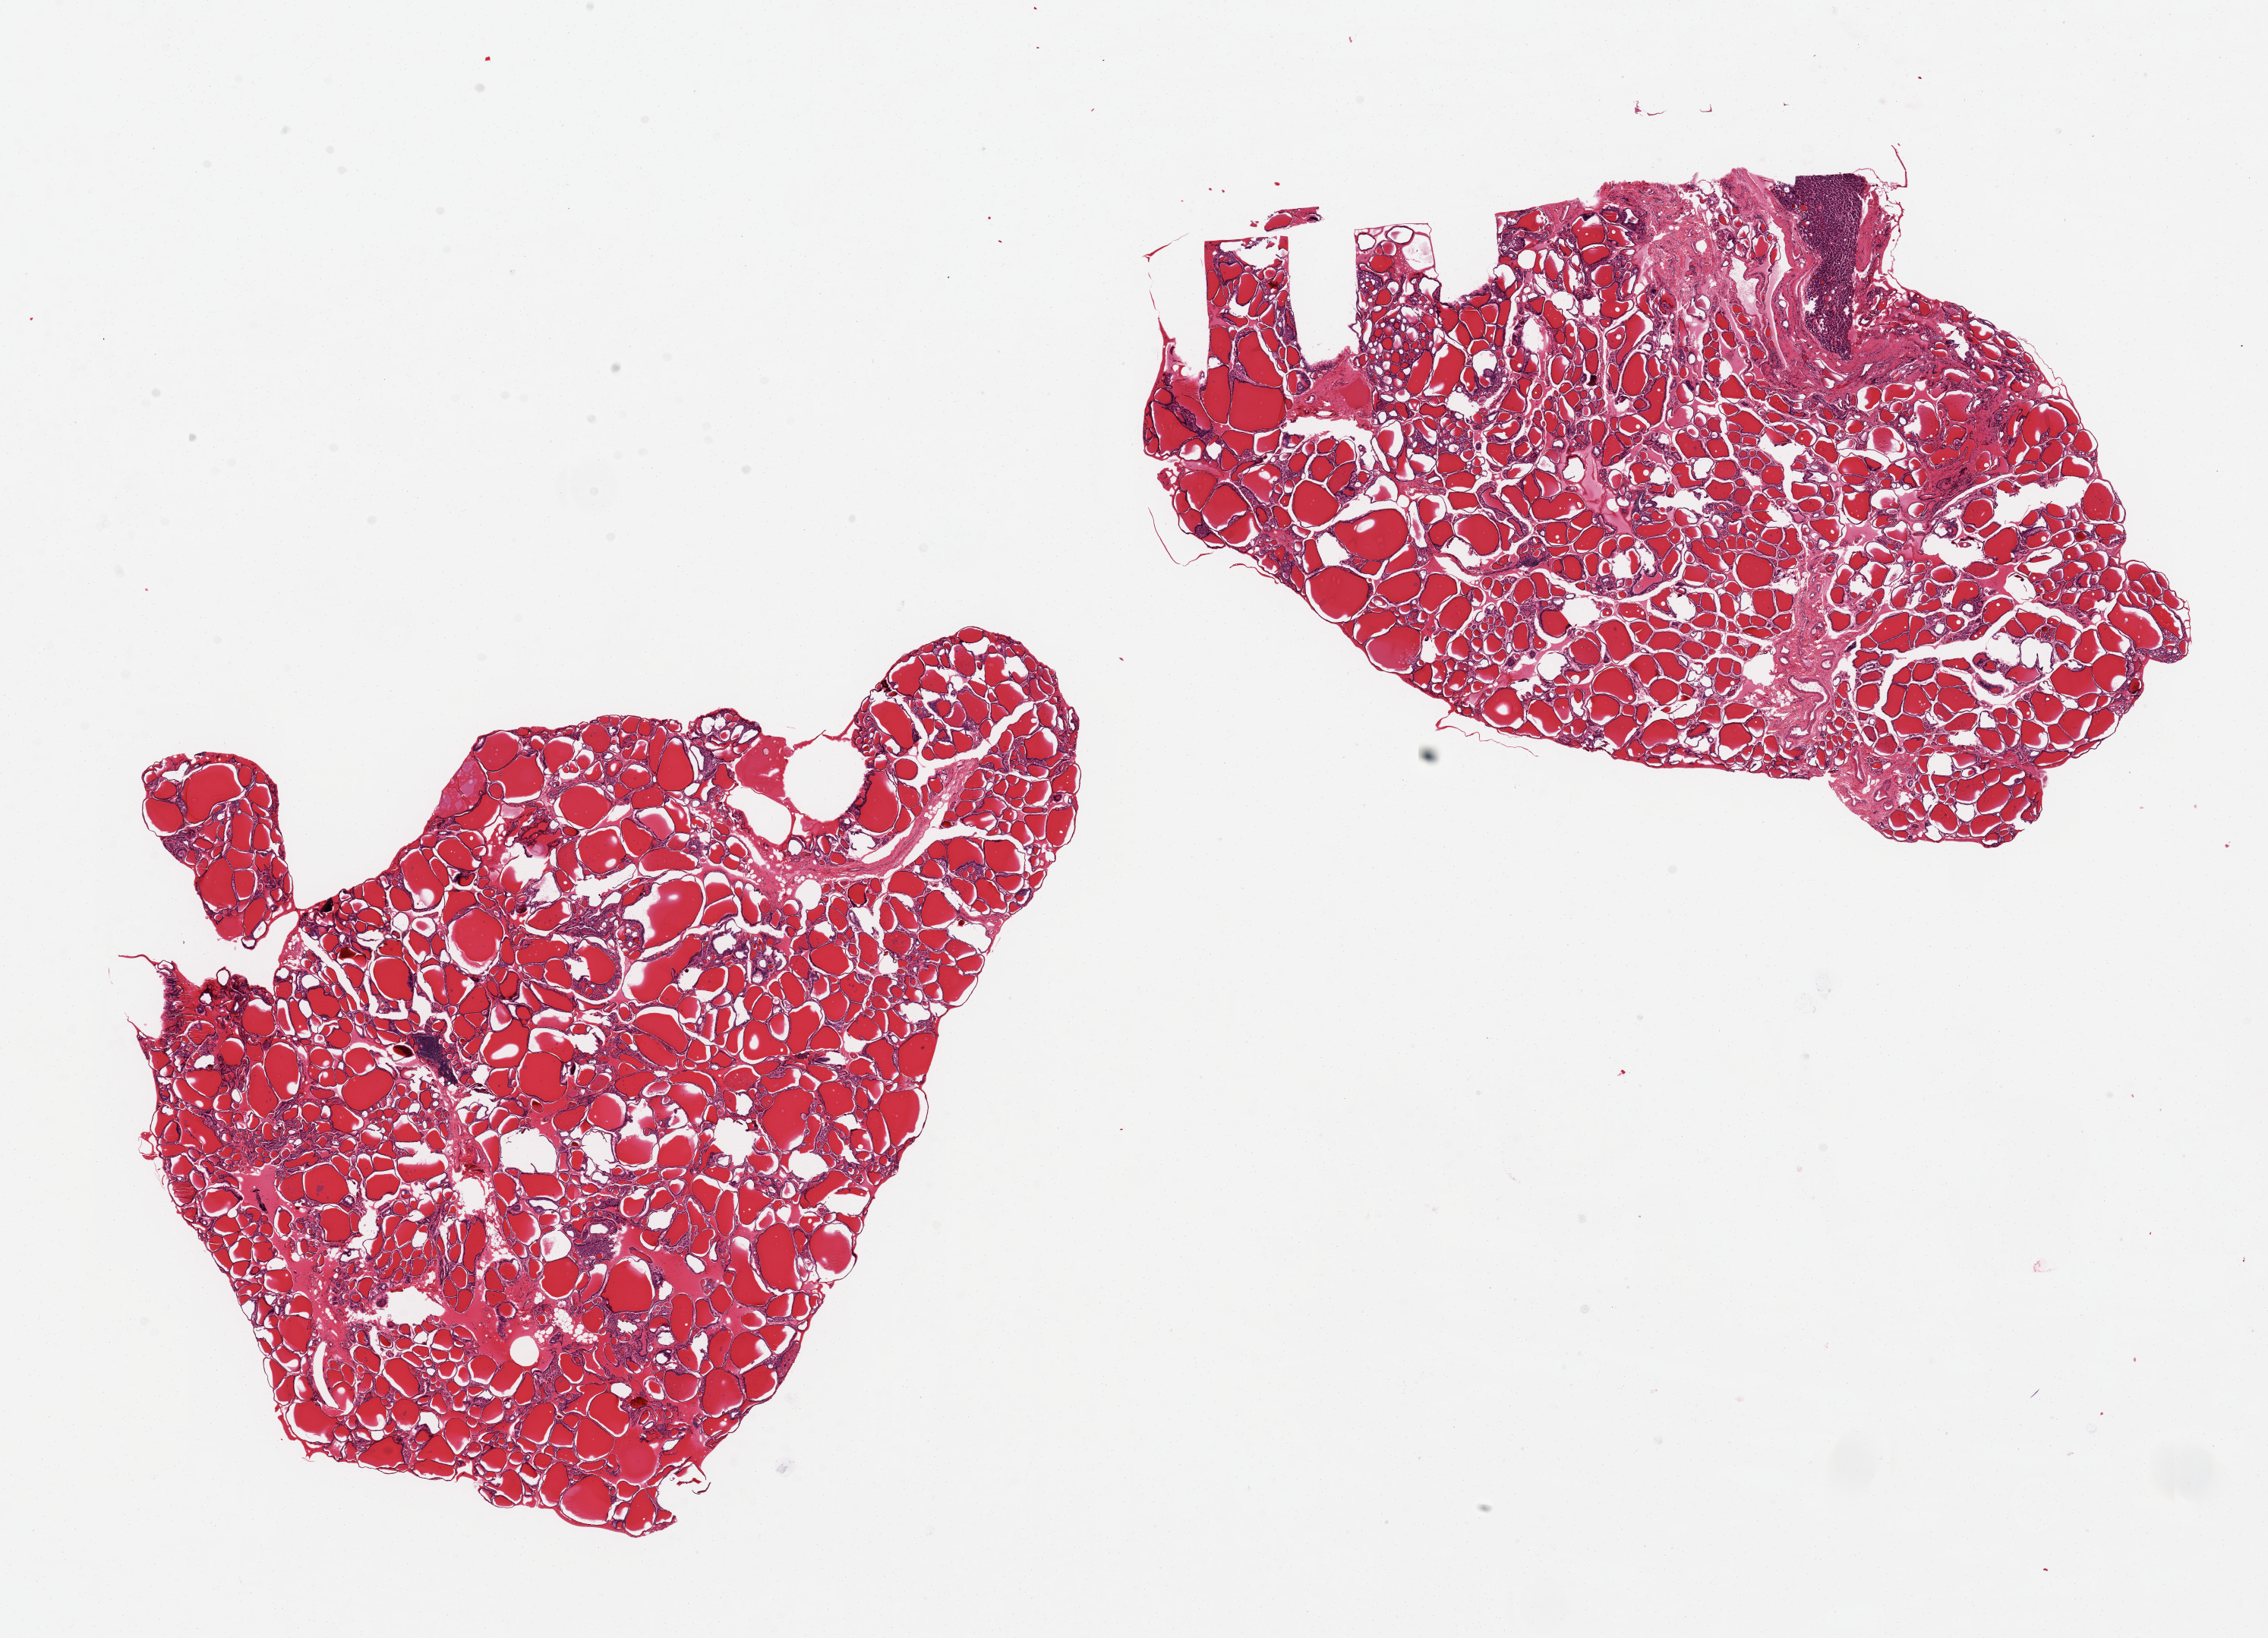
Digitized hematoxylin and eosin (H&E)-stained section, brightfield, shown as a low-resolution overview of the whole scanned area (about 23.6 x 17.1 mm, acquisition: 20x scan), PAXgene-fixed paraffin-embedded (PFPE) section, sampled site (target tissue): thyroid, donor tissue sample. Donor: male.
• reviewer comment on this tissue sample: 2 aliquots, ~10x6mm. Small parathyroid gland fragment, 2mm on one edge. Focal lymphocytic thyroiditis